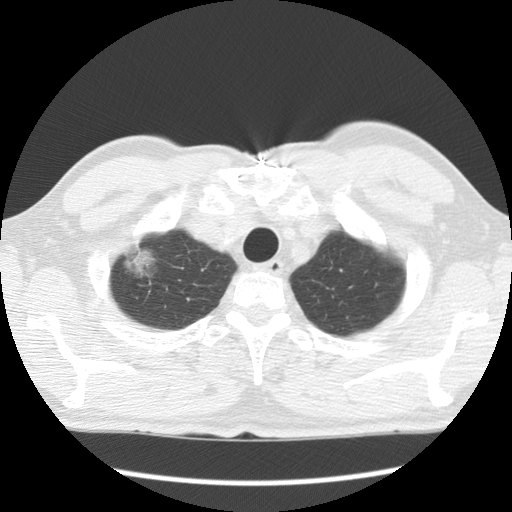
Low-dose screening chest CT, axial slice. Baseline annual screen. Lung window (W 1500 / L -600 HU). 2.5 mm slice thickness. Standard (soft-tissue) reconstruction kernel (STANDARD). Slice 13 of 132 in the series. 512 × 512 image matrix, field of view 340 × 340 mm. Male participant, aged 64 years at enrolment. Former smoker at enrolment.
Expert reader's lesion annotation, box from (x=109, y=221) to (x=169, y=284) px. The screening reader recorded 2 non-calcified nodules or masses ≥4 mm on this exam (right upper lobe, left upper lobe); which of them this box marks is not recorded. Official screen result: positive, change unspecified: nodule(s) >= 4 mm or enlarging nodule(s), mass(es), or other non-specific abnormalities suspicious for lung cancer. Lung cancer was diagnosed 750 days after this screen (after the third annual screen): adenocarcinoma, NOS, right upper lobe, well differentiated (G1), stage IB (AJCC 6th edition), 45 mm at pathology.